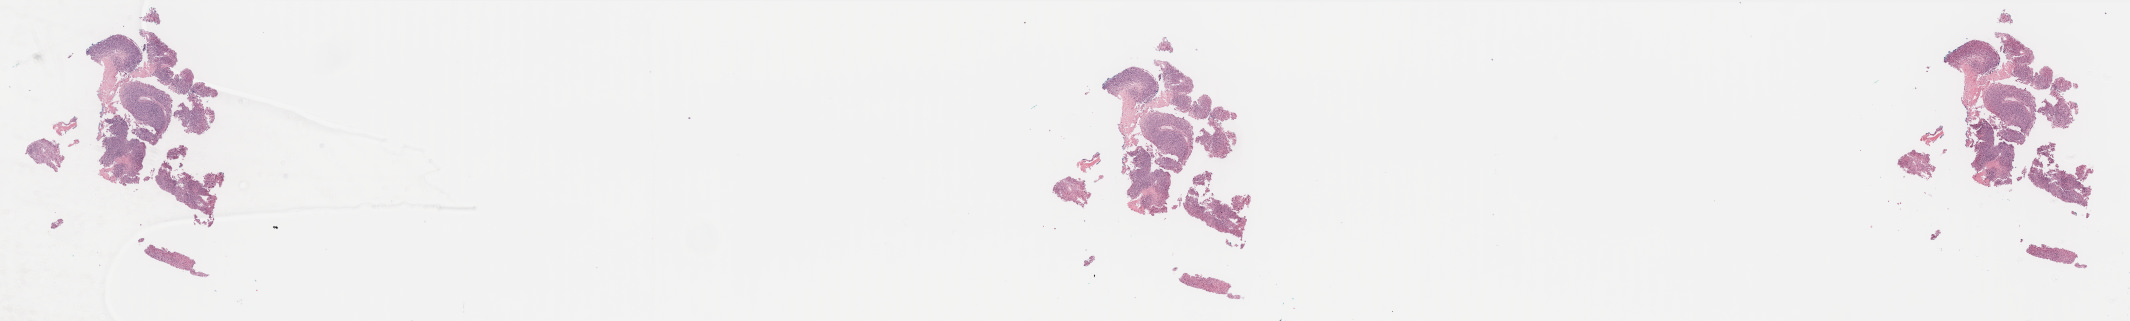
H&E whole-slide image — shown as a low-resolution overview of the whole scanned area (about 34.2 x 5.1 mm, from a 40x scan); FFPE section; primary tumour sample from the skin. Patient: male, age at initial diagnosis 55 years.
Pathologic diagnosis: Malignant melanoma, NOS.